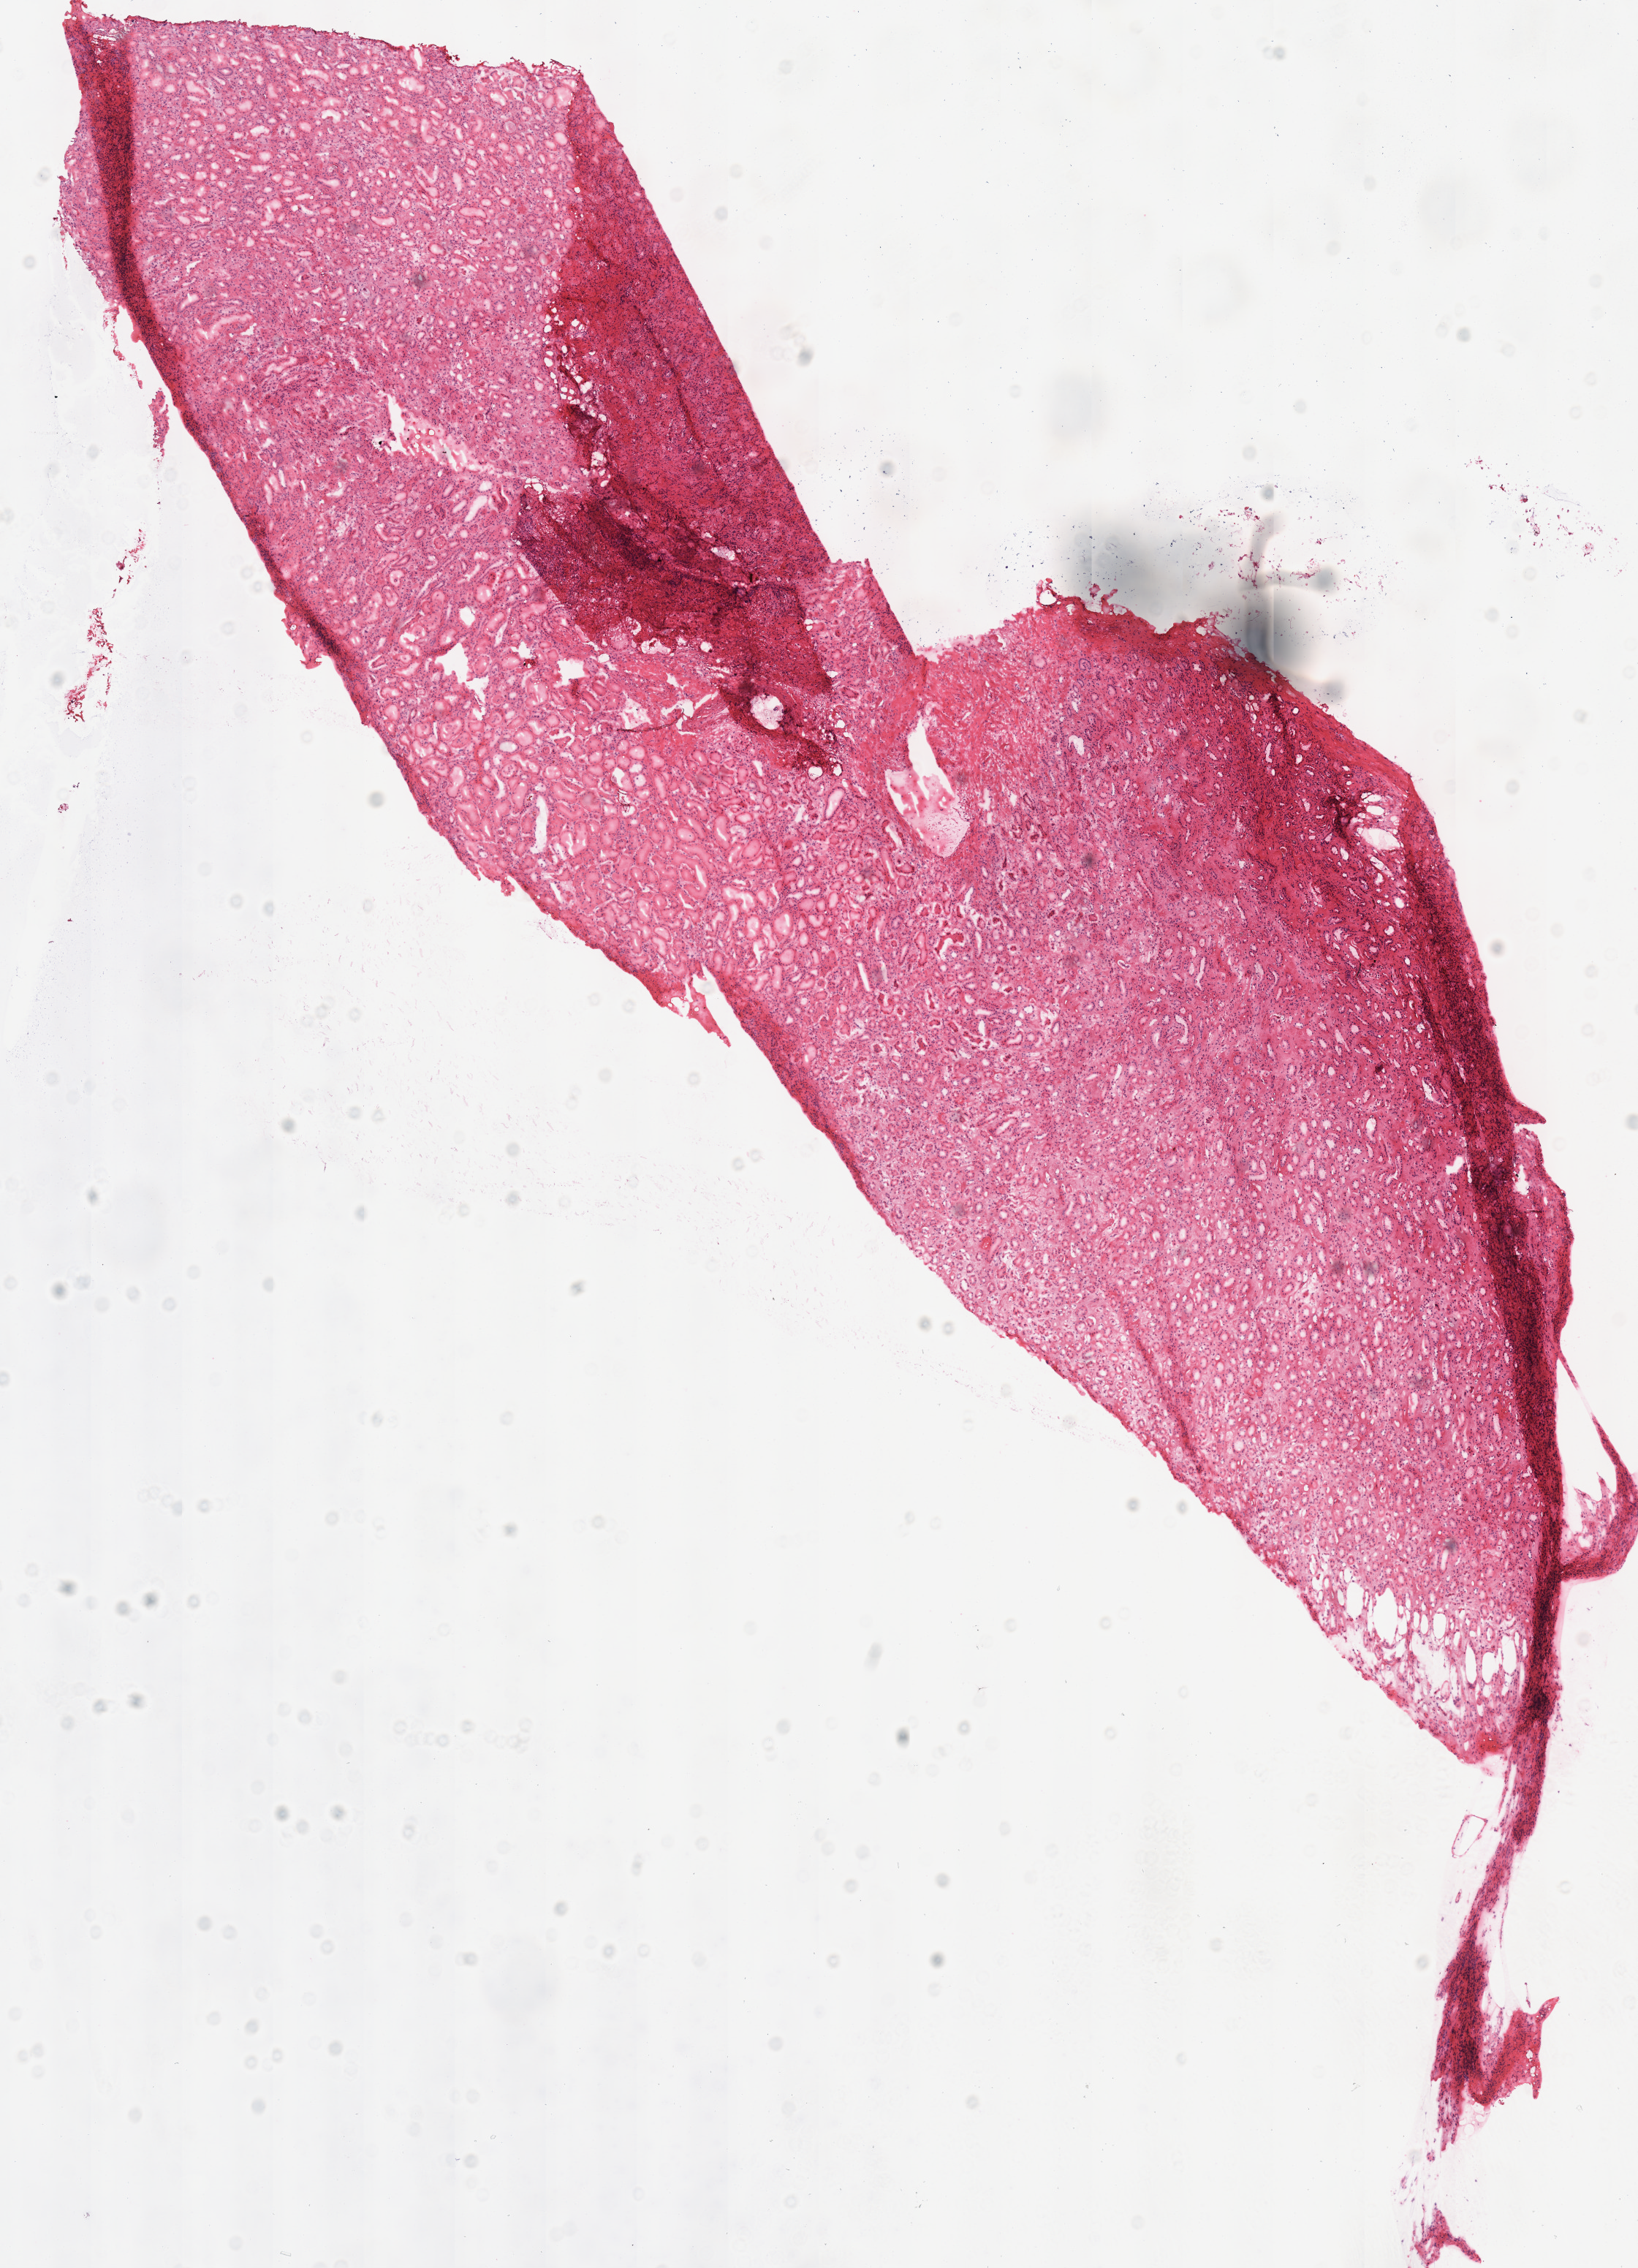
H&E-stained whole-slide image — whole scanned area (about 8.8 x 12.2 mm, from a 40x scan) shown as a low-resolution overview; frozen section from the top of the tissue portion; kidney, solid tissue normal (non-tumour tissue) sample. Male, age 82 years at initial diagnosis. Infiltration values recorded for this section: lymphocyte infiltration 0%, monocyte infiltration 0%, neutrophil infiltration 0%.
This section: solid tissue normal (non-tumour) sample from the same patient. Patient diagnosis: Papillary adenocarcinoma, NOS.